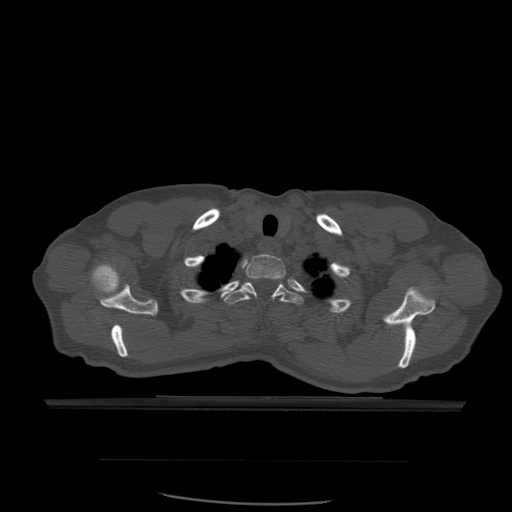
CT including the spine, one axial slice. Slice 462 of 574 in the series (ordered by position). Bone window (W 1800 / L 400 HU). 1.25 mm slice thickness. 512 × 512 image matrix. Patient age 48 years. From the clinical record (not read from this slice): primary cancer: lung; vertebrae with lytic lesions (as recorded): T11.
Outlined on this slice (semi-automatic segmentation, software-assisted and operator-edited):
- T1 vertebra: bounding box <246,254,286,301> (left, top, right, bottom; pixels)
- T2 vertebra: <224,281,303,309>